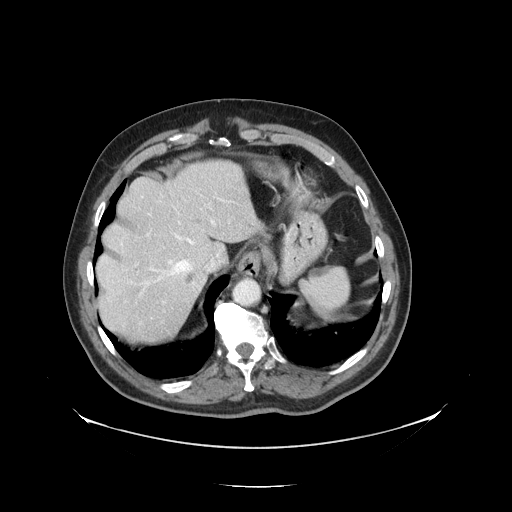
Contrast-enhanced abdominal CT, one axial slice. Position 109 of 138 along the scan axis. Reconstruction kernel STANDARD. 120 kVp. Intravenous contrast given. Soft-tissue window (W 400 / L 40 HU). 2.5 mm slice thickness. 512 × 512 image matrix, field of view 497 × 497 mm. Male patient, age 77 years. Case-level facts recorded for this patient, not image findings: diagnosis: colorectal cancer liver metastases, imaged before liver resection; multiple liver metastases: no; largest metastasis: 1.5 cm; disease in both lobes: no.
Structures marked on this image (expert manual segmentation):
- hepatic veins: bounding box <140,203,216,287> (left, top, right, bottom; pixels)
- liver: <98,161,256,343>
- planned liver remnant (the part of the liver to remain after resection): <97,161,257,289>
- portal vein (with intrahepatic branches): <135,187,232,319>
- liver metastasis: <186,277,194,282>